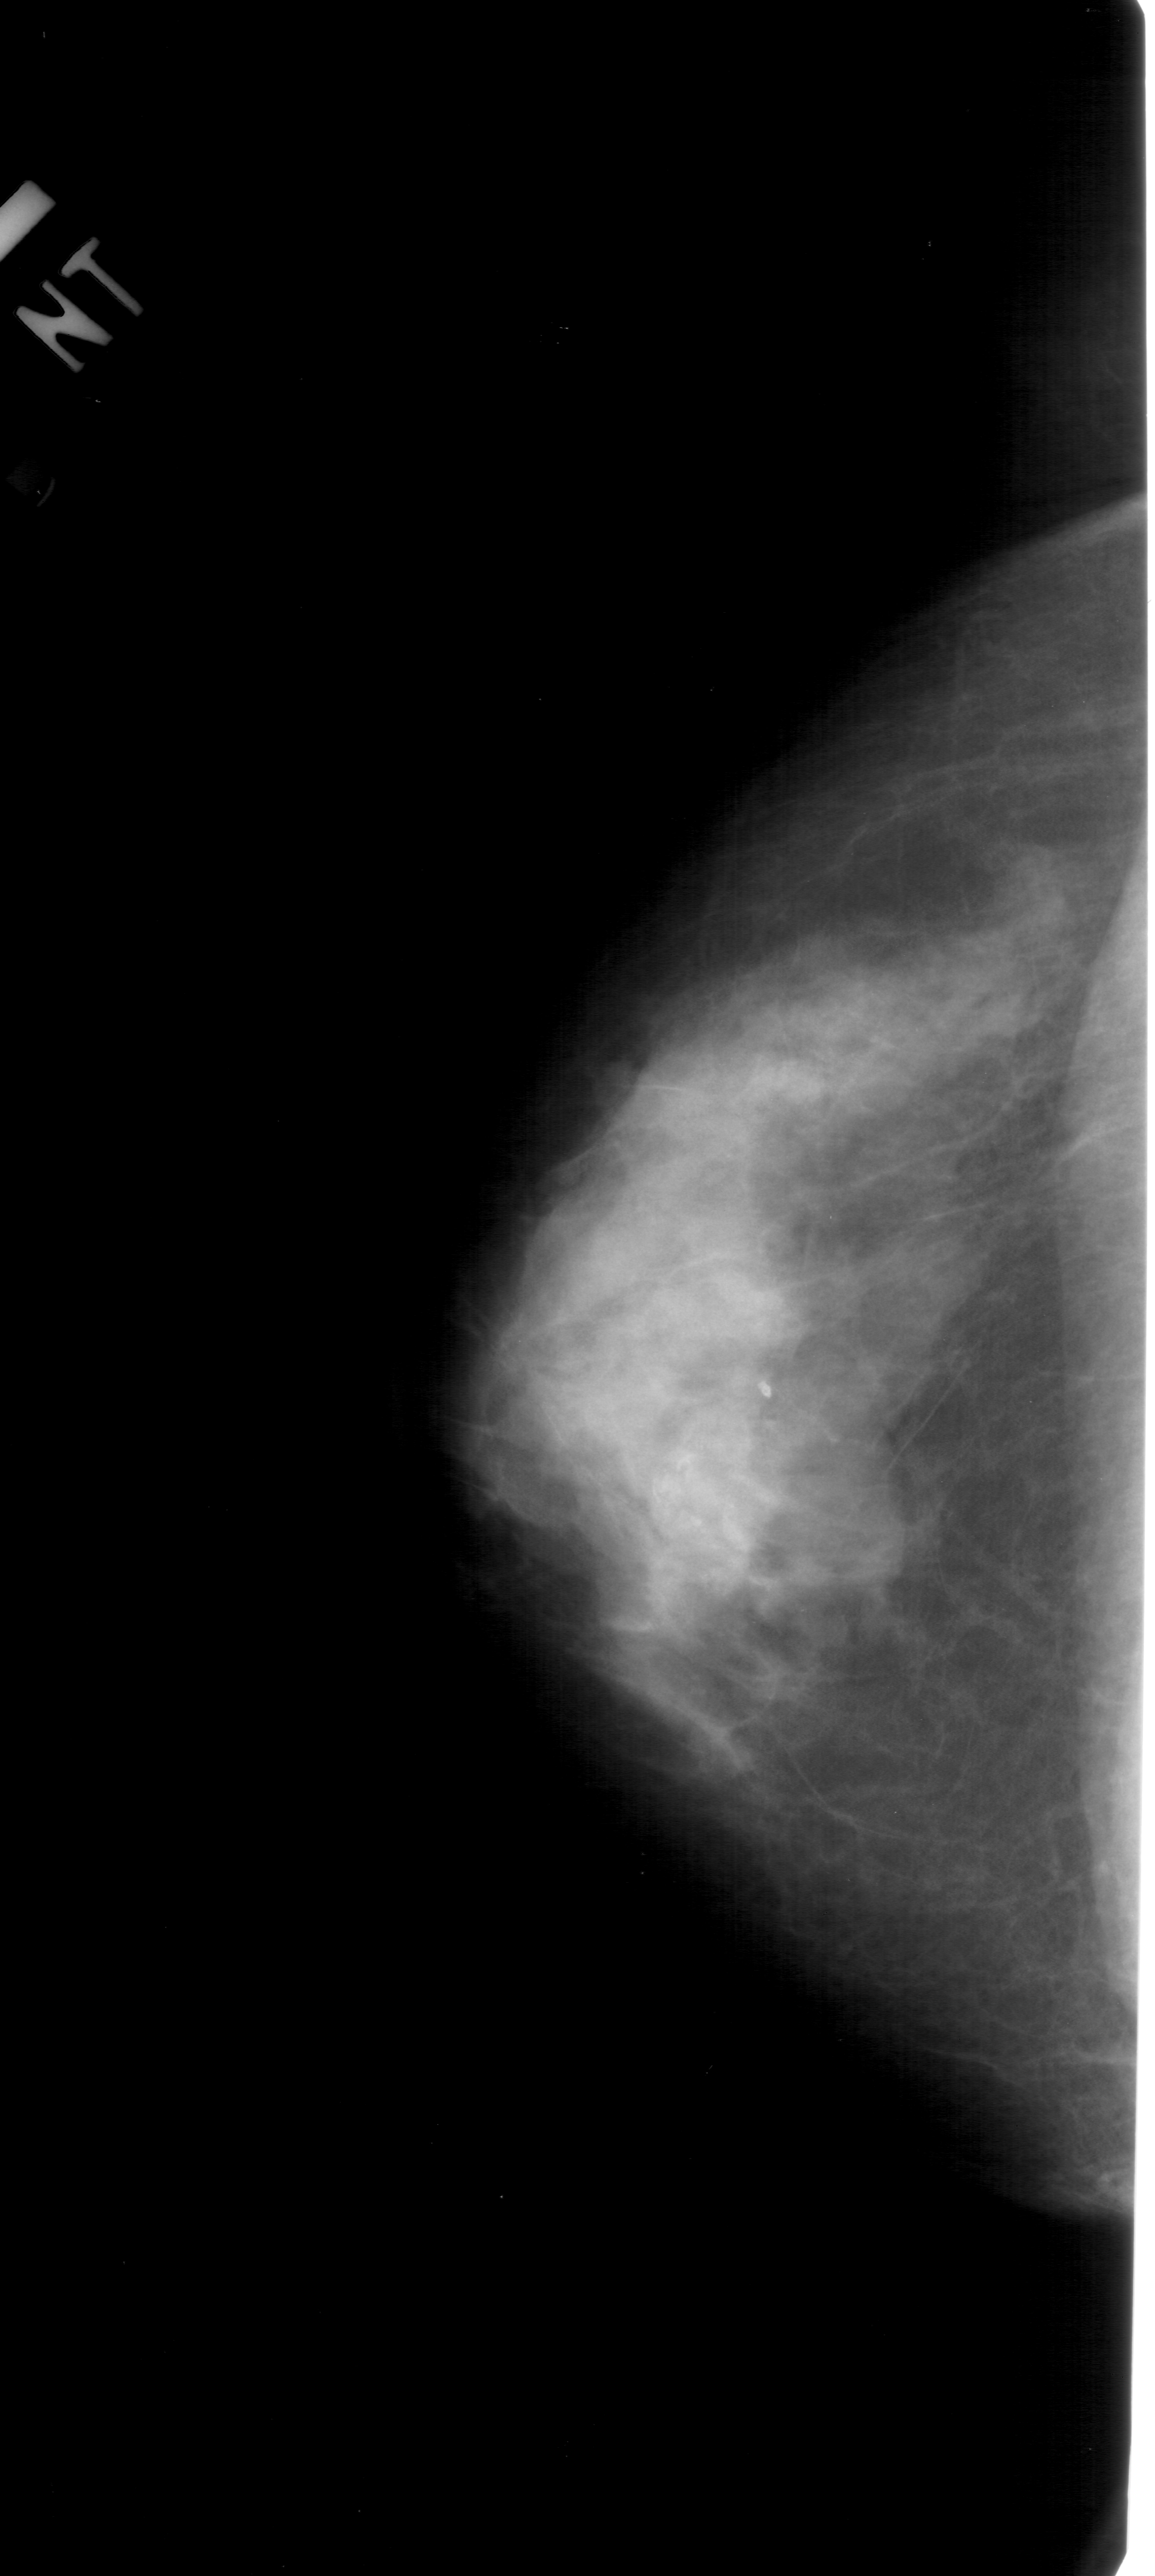
Scanned film-screen mammogram, left breast, craniocaudal (CC) view, breast composition: extremely dense (BI-RADS density category 4 of 4).
Marked abnormality: calcifications, morphology pleomorphic, distribution clustered; BI-RADS assessment category 4; subtlety rating 3 on a 1 (subtle) to 5 (obvious) scale; pathology result (as recorded, not read from the image): malignant.